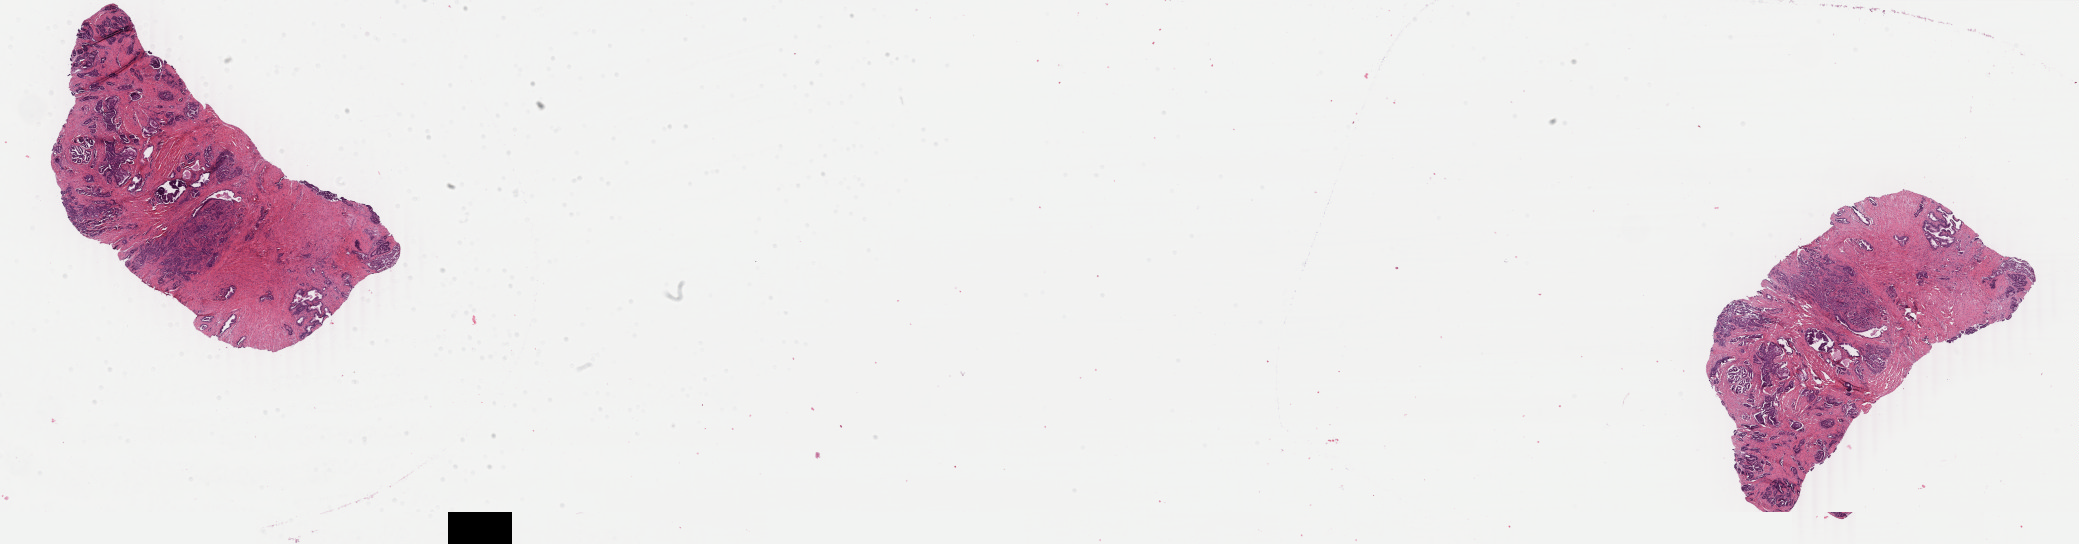
Digitized H&E-stained tissue section (whole slide), a low-resolution overview of the entire scanned area, about 33.1 x 8.7 mm, FFPE section, sample: primary tumour, prostate. Patient: male, age at initial diagnosis 63 years. Gleason score: 7 (3+4).
• lymph nodes positive (case pathology): 0 of 19 examined
• laterality: bilateral
• pathologic diagnosis: Adenocarcinoma, NOS (prostate gland)